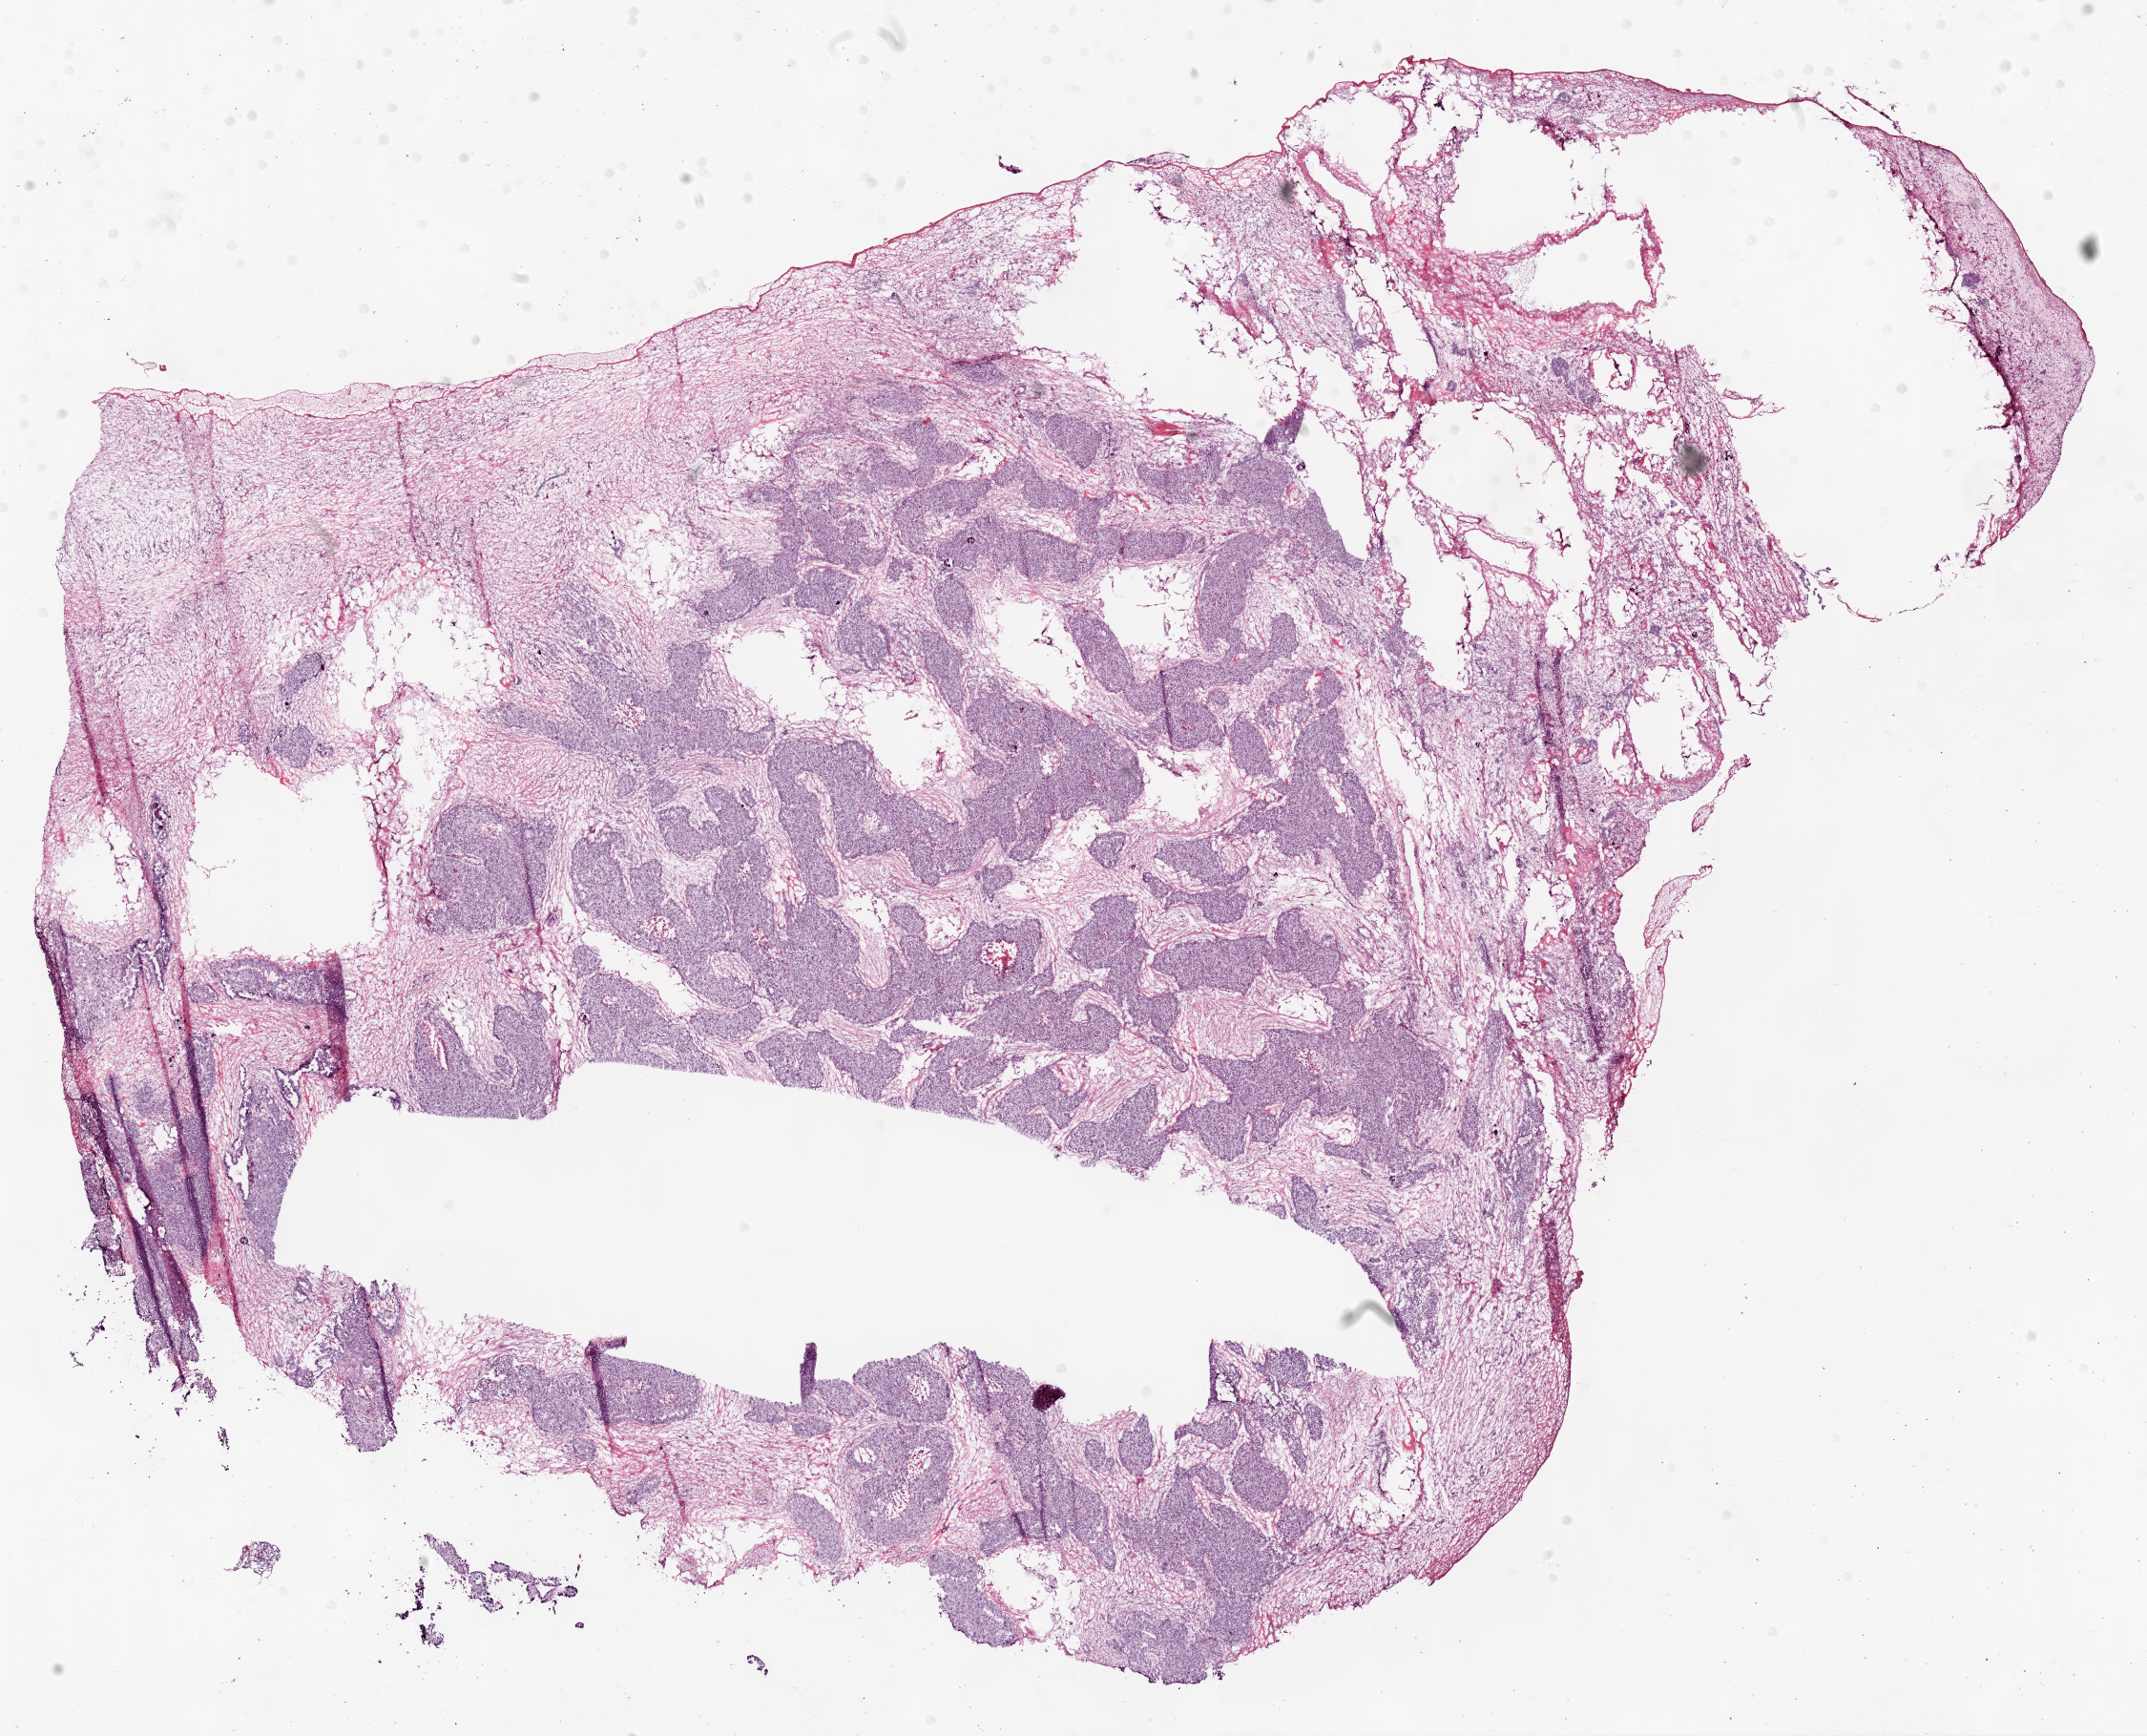
Whole-slide histology image, H&E-stained, a low-resolution overview of the entire scanned area, about 18.1 x 14.6 mm. Frozen section from the bottom of the tissue portion. Sample: primary tumour, ovary. Patient: female, age at initial diagnosis 53 years. Histologic grade: G3 (poorly differentiated). Slide review estimates, as recorded: tumour cells 50%, tumour nuclei 70%, normal cells 0%, stromal cells 45%, necrosis 5%.
FIGO stage: IIIC. Pathologic diagnosis: Serous cystadenocarcinoma, NOS. Laterality: bilateral.